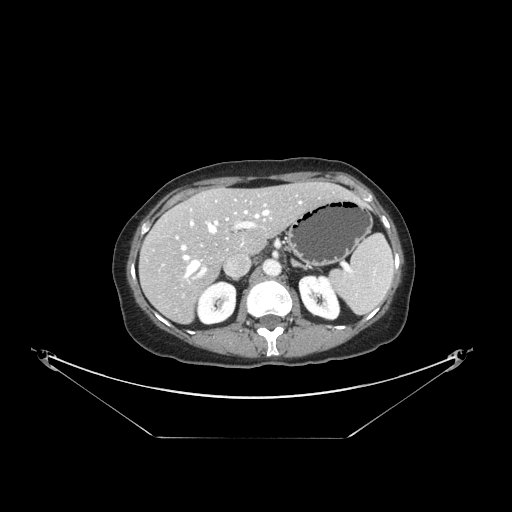
Contrast-enhanced abdominal CT, one axial slice; slice 94 of 148 in the series (ordered by position); intravenous contrast given; soft-tissue window (W 400 / L 40 HU); 2.5 mm slice thickness; 512 × 512 image matrix, field of view 500 × 500 mm. Female patient, age 73 years. From the clinical record (not read from this slice): diagnosis: colorectal cancer liver metastases, imaged before liver resection; multiple liver metastases: no; largest metastasis: 1 cm; disease in both lobes: no.
Annotated regions visible in this slice (outlined manually by an expert reader):
- hepatic veins: box from (x=183, y=202) to (x=301, y=277) px
- liver: (x=140, y=182)–(x=351, y=322)
- planned liver remnant (the part of the liver to remain after resection): (x=169, y=183)–(x=352, y=255)
- portal vein (with intrahepatic branches): (x=176, y=204)–(x=266, y=278)